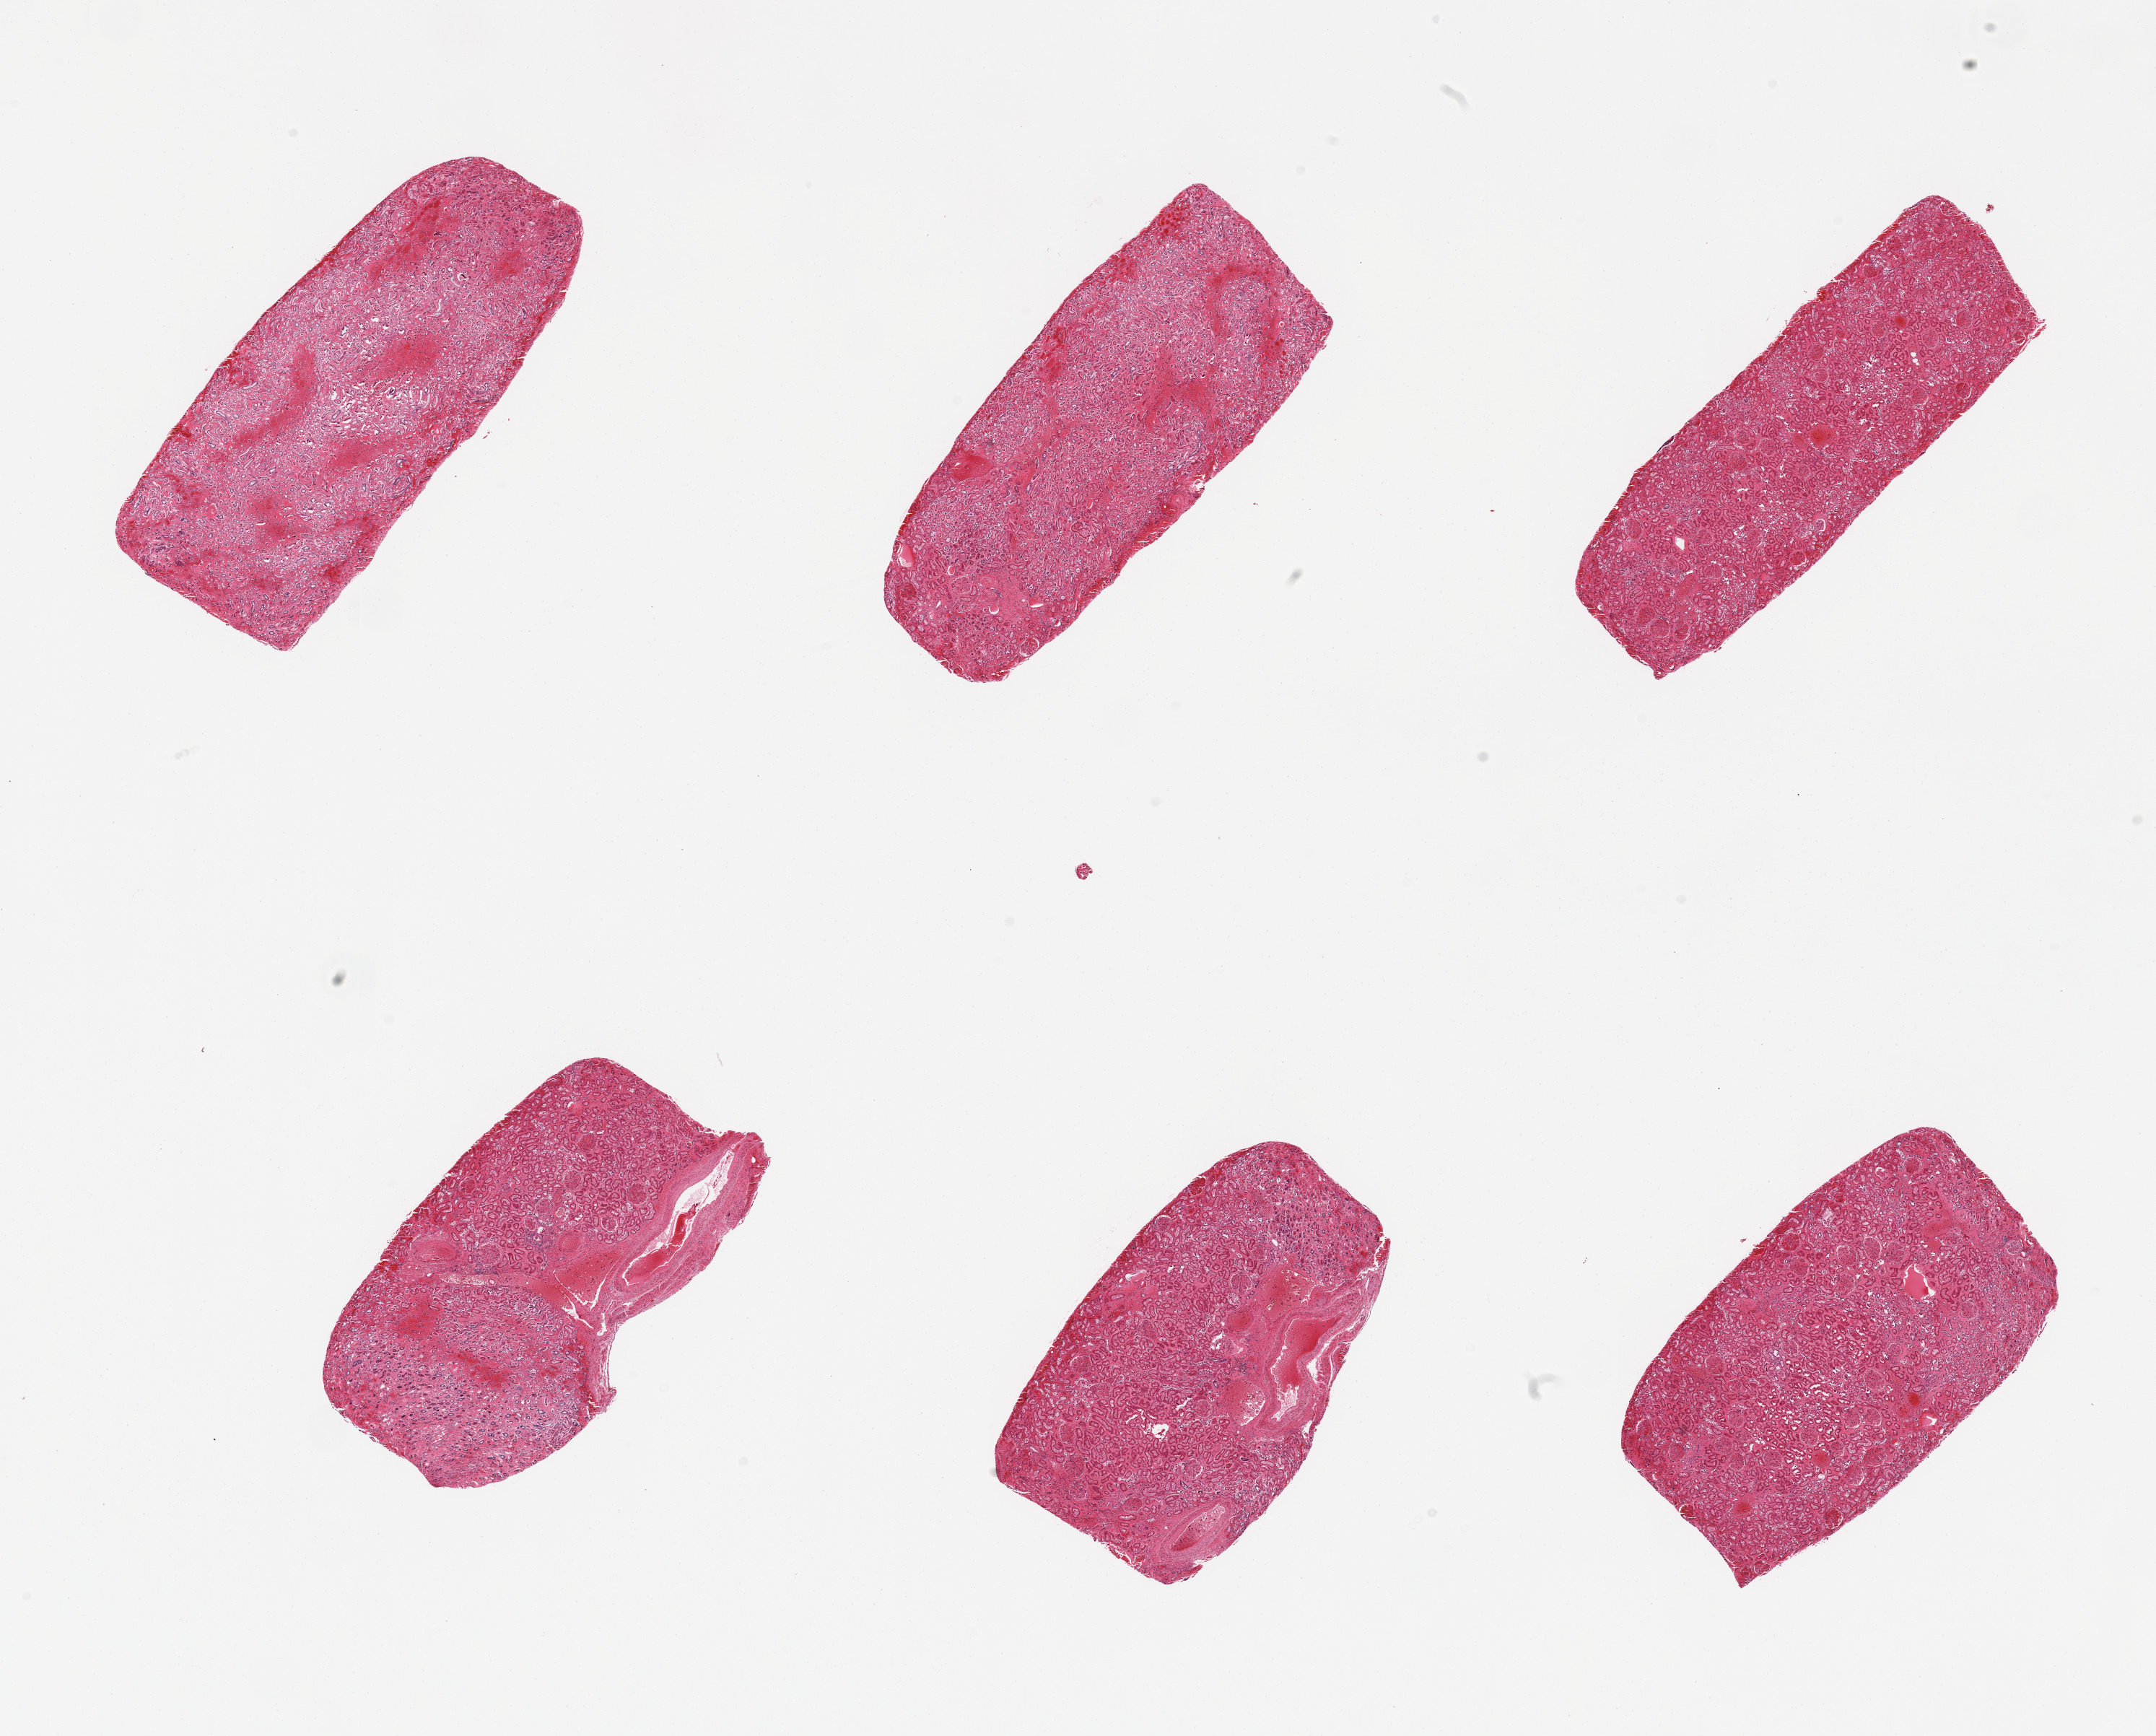
Whole-slide image, haematoxylin and eosin stain, a low-resolution overview of the entire scanned area, about 23.6 x 19.0 mm (acquisition: 20x scan). PAXgene-fixed paraffin-embedded (PFPE) section. Target tissue: renal cortex. Donor tissue sample. Donor: male.
Pathologist's review note for this sample: 6 pieces, cortex and medulla, few sclerotic glomeruli.